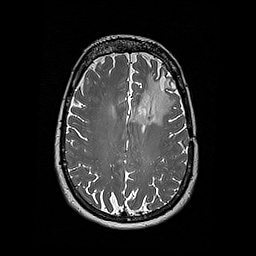
Brain MRI from a brain-tumour surgery series, one axial slice. Slice 122 of 192 in the series (ordered by position). 1 mm slice thickness. 256 × 256 image matrix, field of view 250 × 250 mm. From the clinical record (not read from this slice): histopathology: Oligodendroglioma; WHO grade: 2; IDH mutation: yes; tumour location: Left Frontal.
Outlined on this slice (outlined manually by an expert reader):
- tumour: box from (x=137, y=74) to (x=174, y=125) px